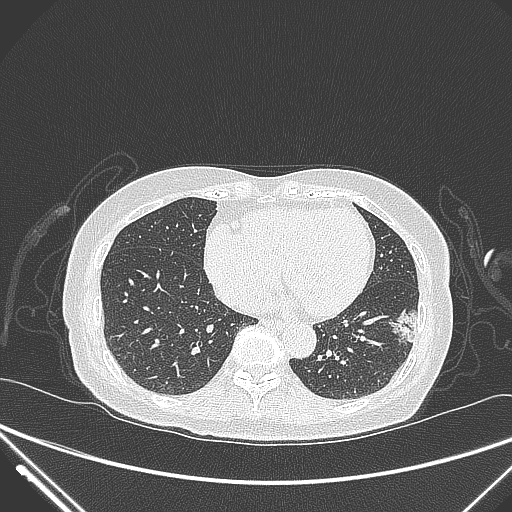
Chest CT, one axial slice. Slice 107 of 310 in the series (ordered by position). Lung window (W 1500 / L -600 HU). 512 × 512 image matrix, field of view 377 × 377 mm. Patient: female, 82 years. Case-level facts recorded for this patient, not image findings: clinical TNM (as recorded): T1c N0 M0; histopathological grade: G2.
Outlined on this slice (bounding box drawn by a radiologist):
- lung tumour (recorded histology: adenocarcinoma): bounding box <387,306,422,351> (left, top, right, bottom; pixels)